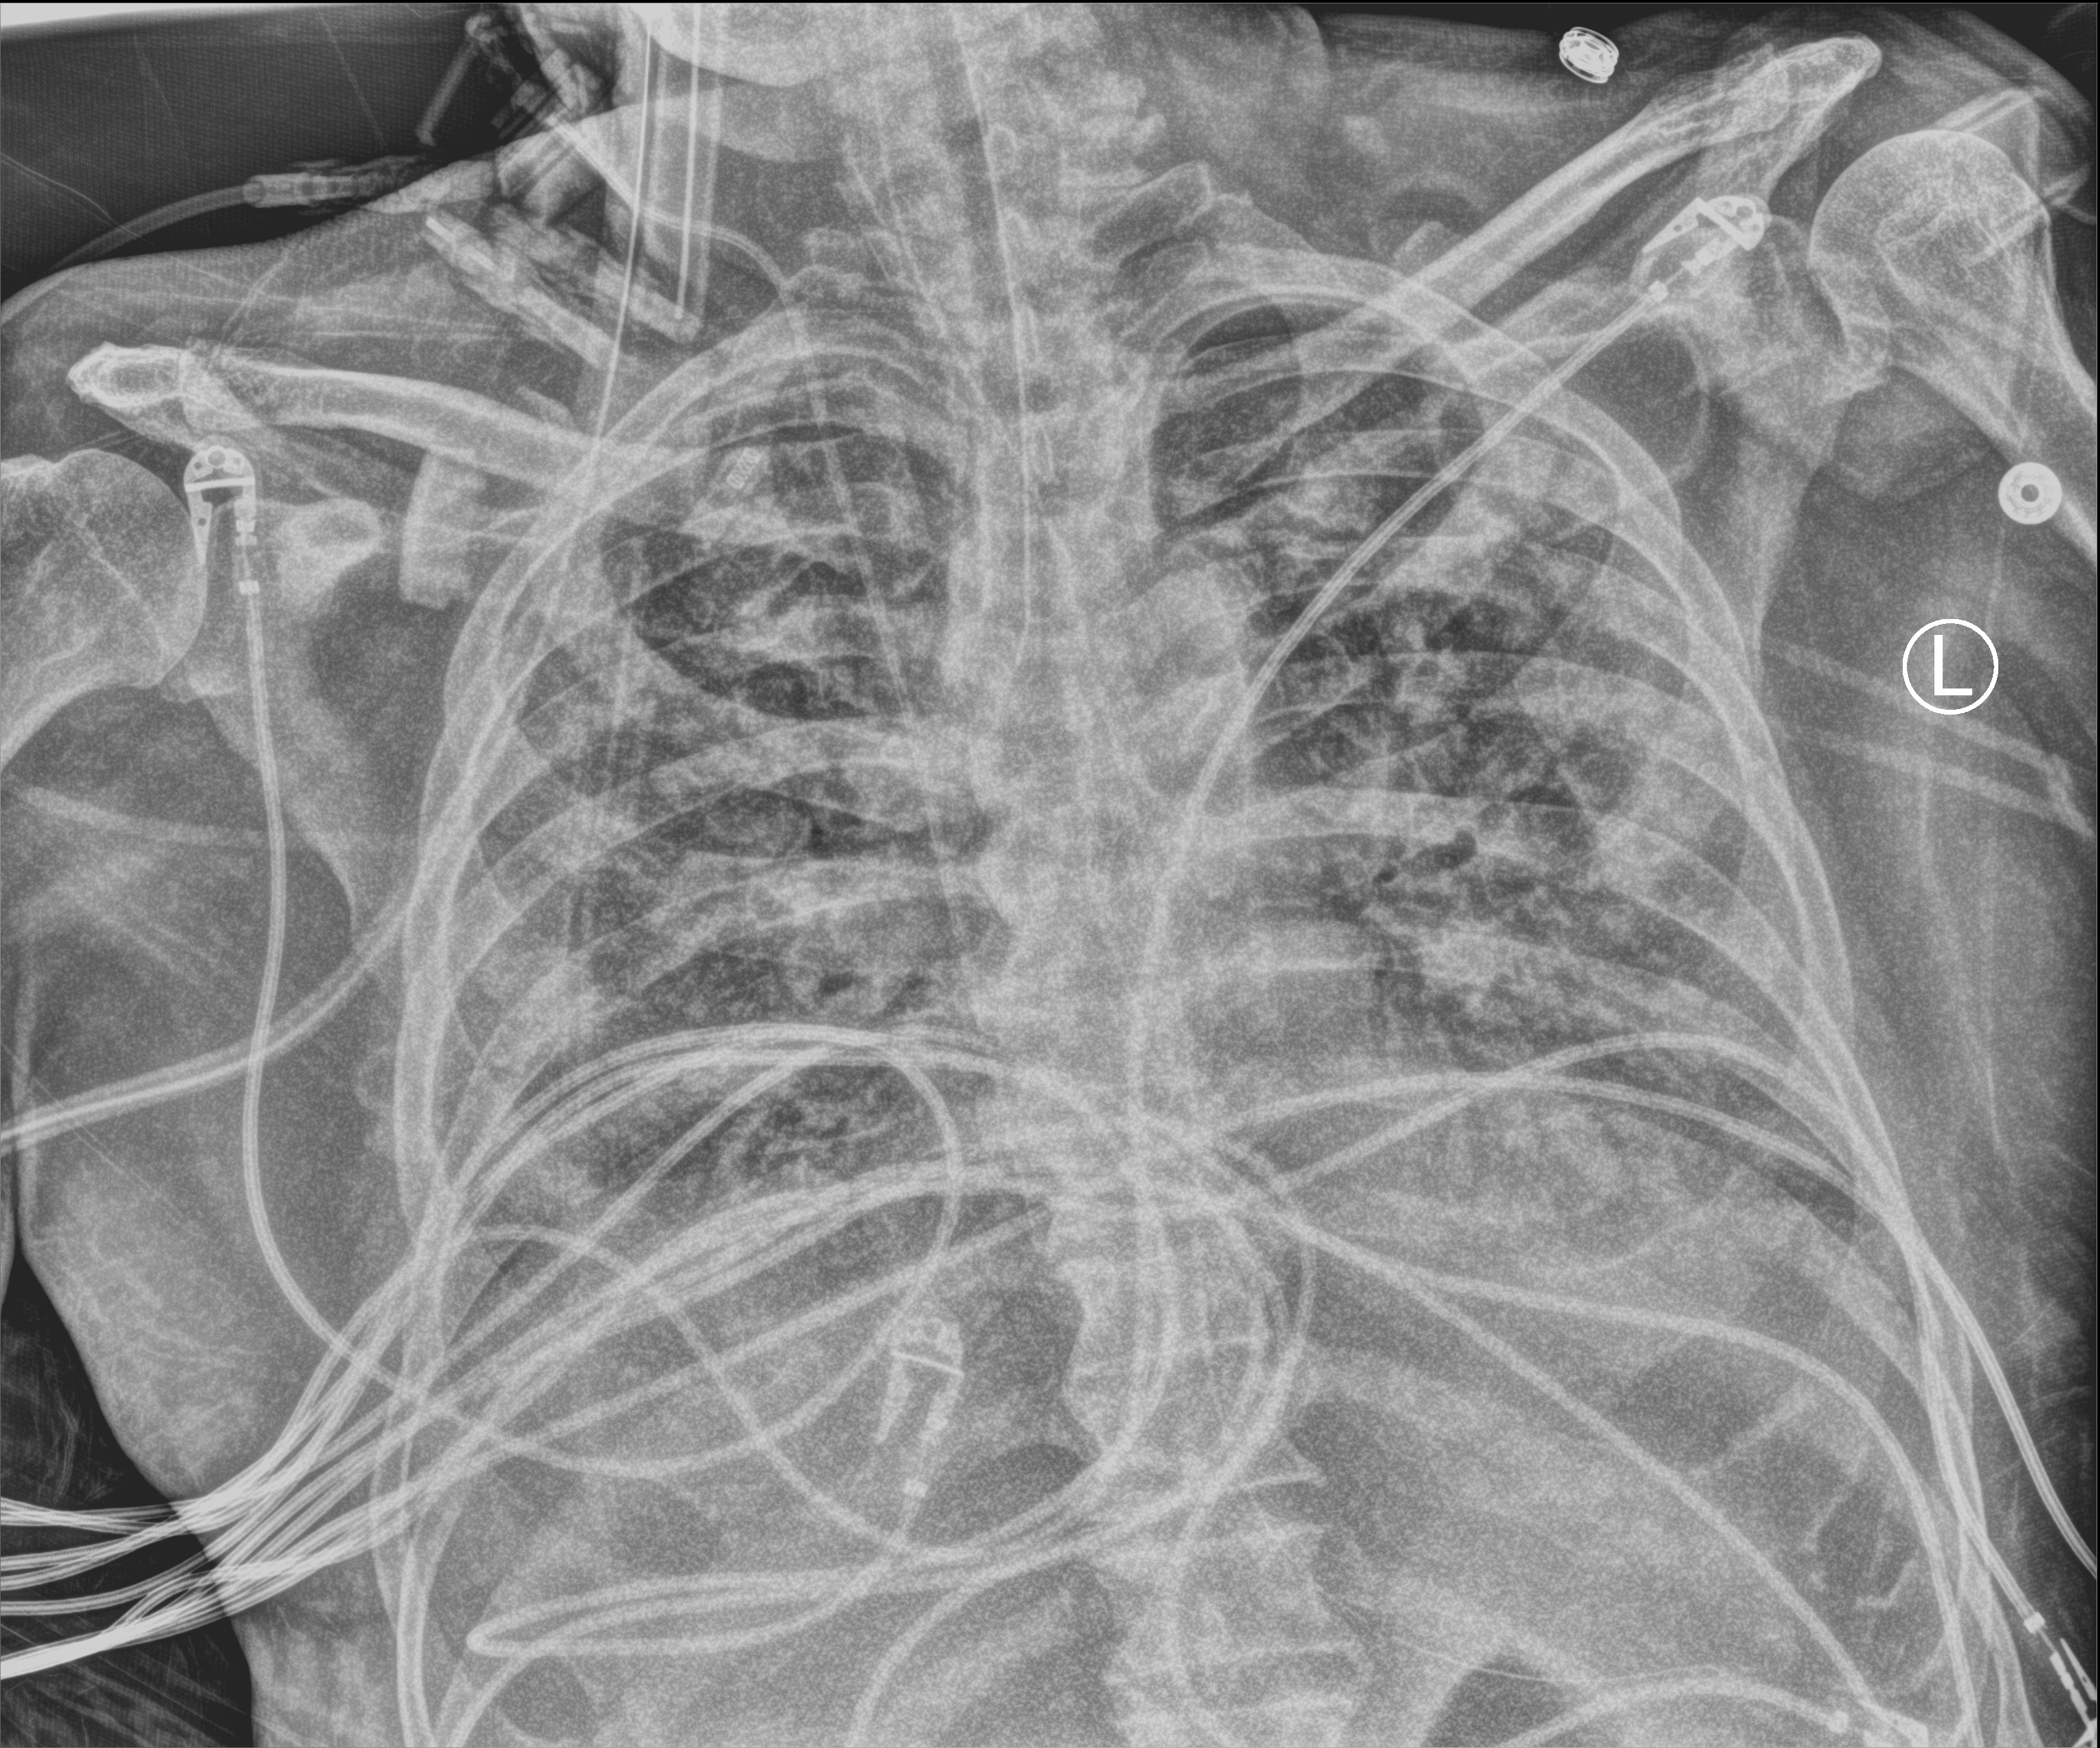
Chest X-ray (portable); anteroposterior (AP) projection. Patient hospitalised with COVID-19; male, aged 75–90 years.
Hospital-stay facts (about this admission, not read from this image; timing relative to this image not recorded):
- mechanically ventilated during this hospital stay: yes
- diabetes (admission record): no
- admitted to intensive care during this hospital stay: yes